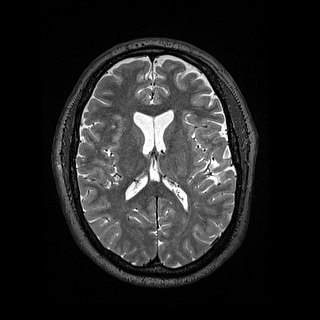
Brain MRI from a brain-tumour surgery series, one axial slice. Position 74 of 144 along the scan axis. 320 × 320 image matrix. Case-level facts recorded for this patient, not image findings: histopathology: Astrocytoma; WHO grade: 2; IDH mutation: yes; tumour location: Left Insular.
Outlined on this slice (manually delineated by an expert):
- tumour: box from (x=196, y=158) to (x=208, y=170) px